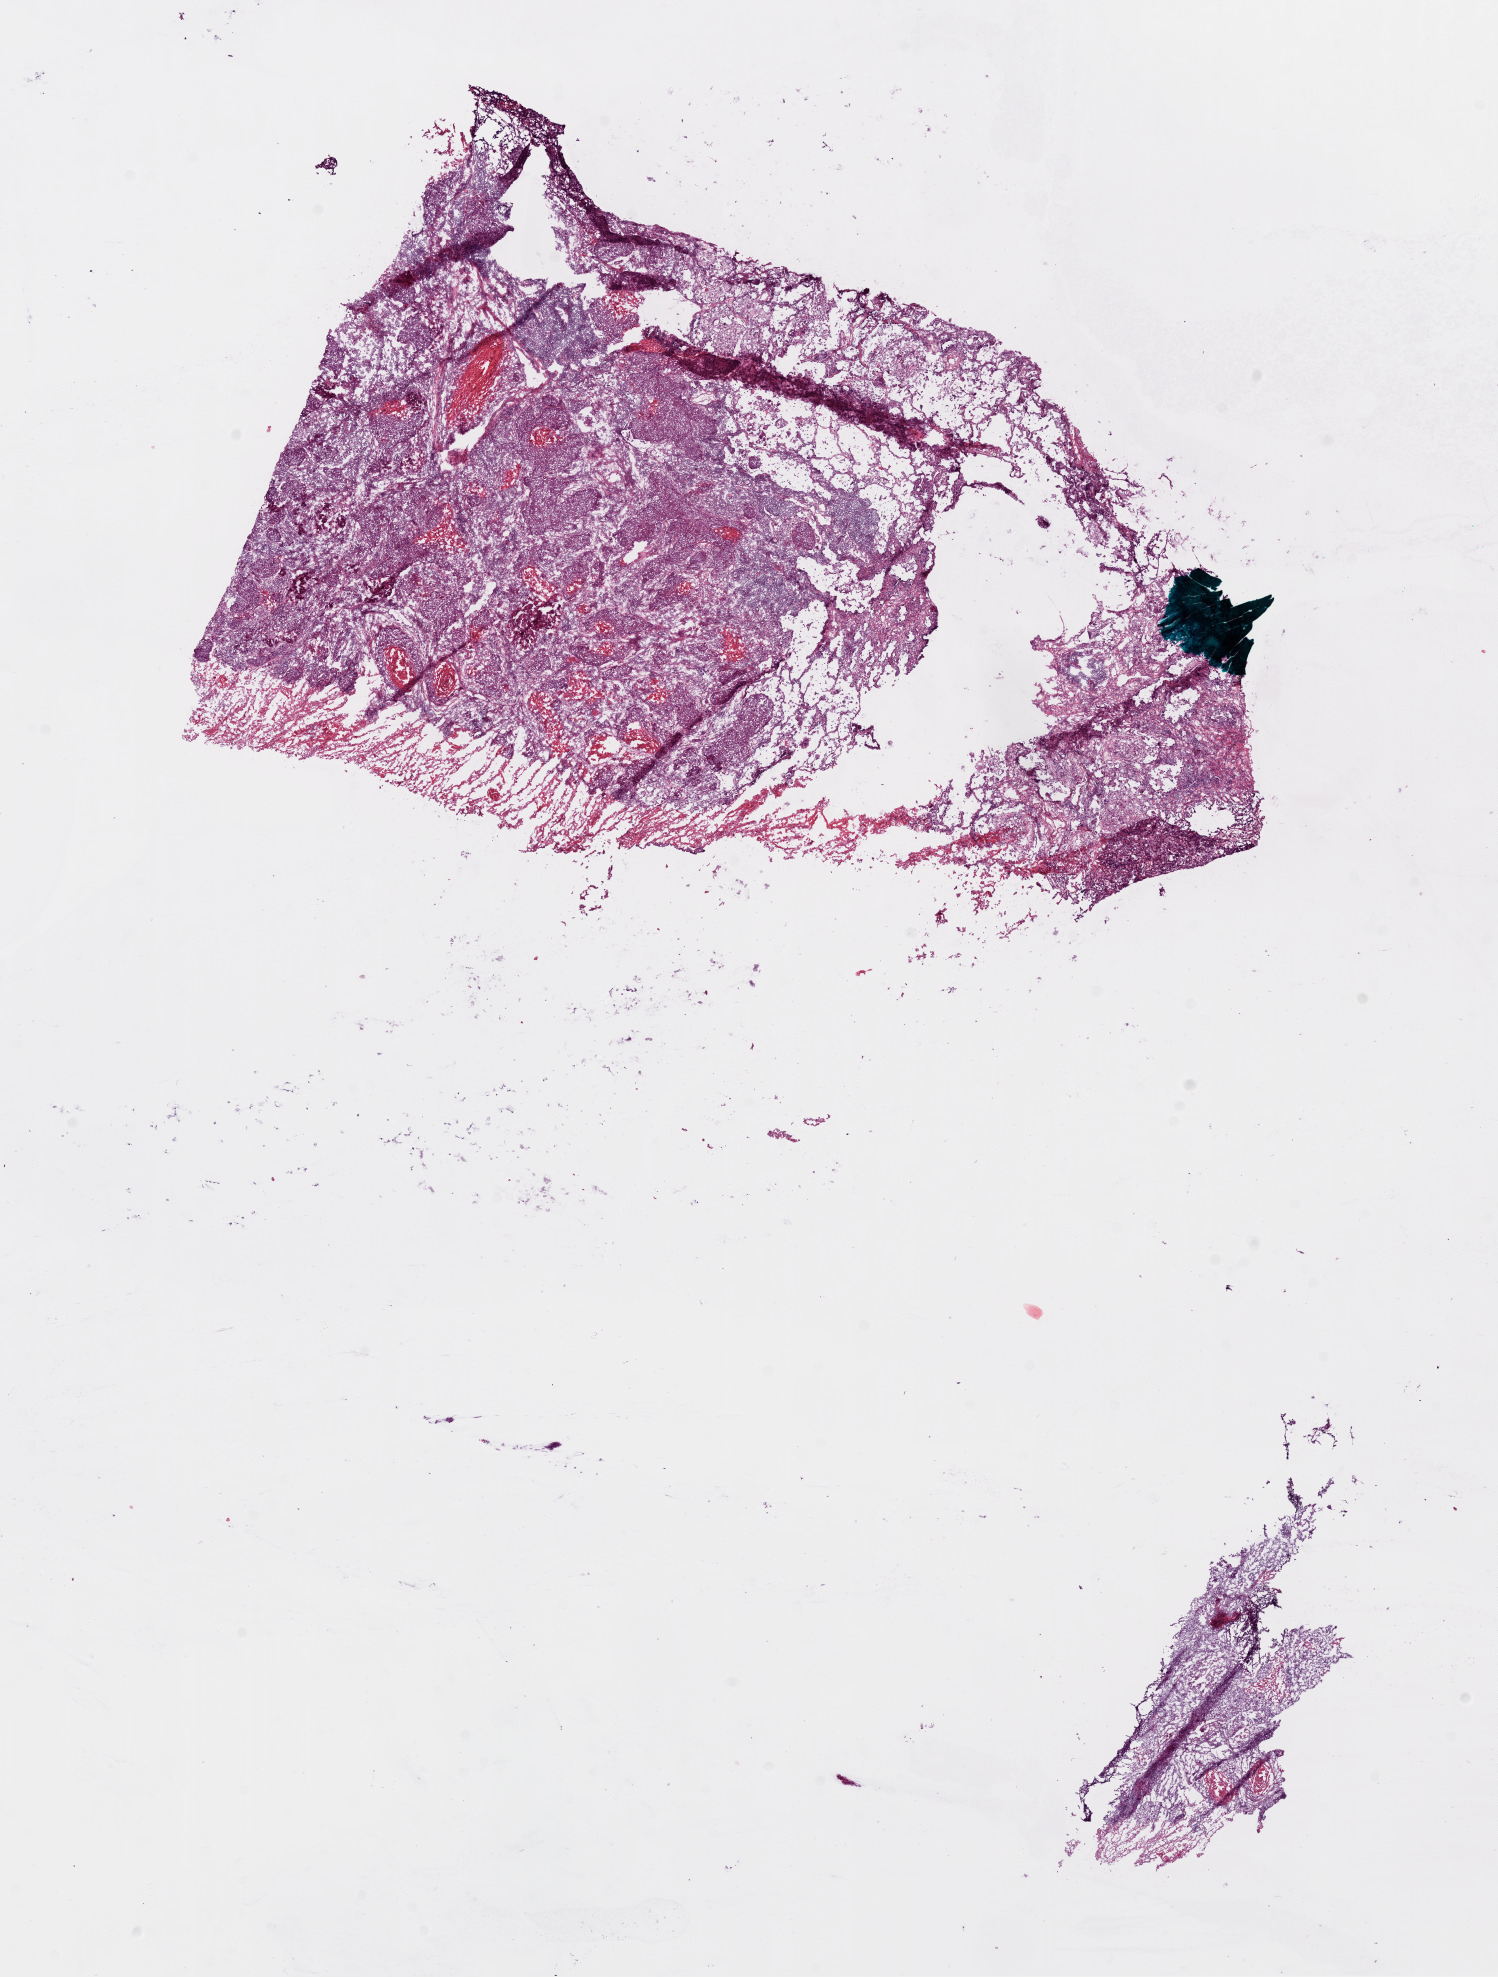
H&E-stained whole-slide image — low-resolution overview of the scanned area, about 12.1 x 16.0 mm, frozen section, lung, primary tumour sample. Female, age 54 years at initial diagnosis.
Diagnosis: Squamous cell carcinoma, NOS (lower lobe, lung).